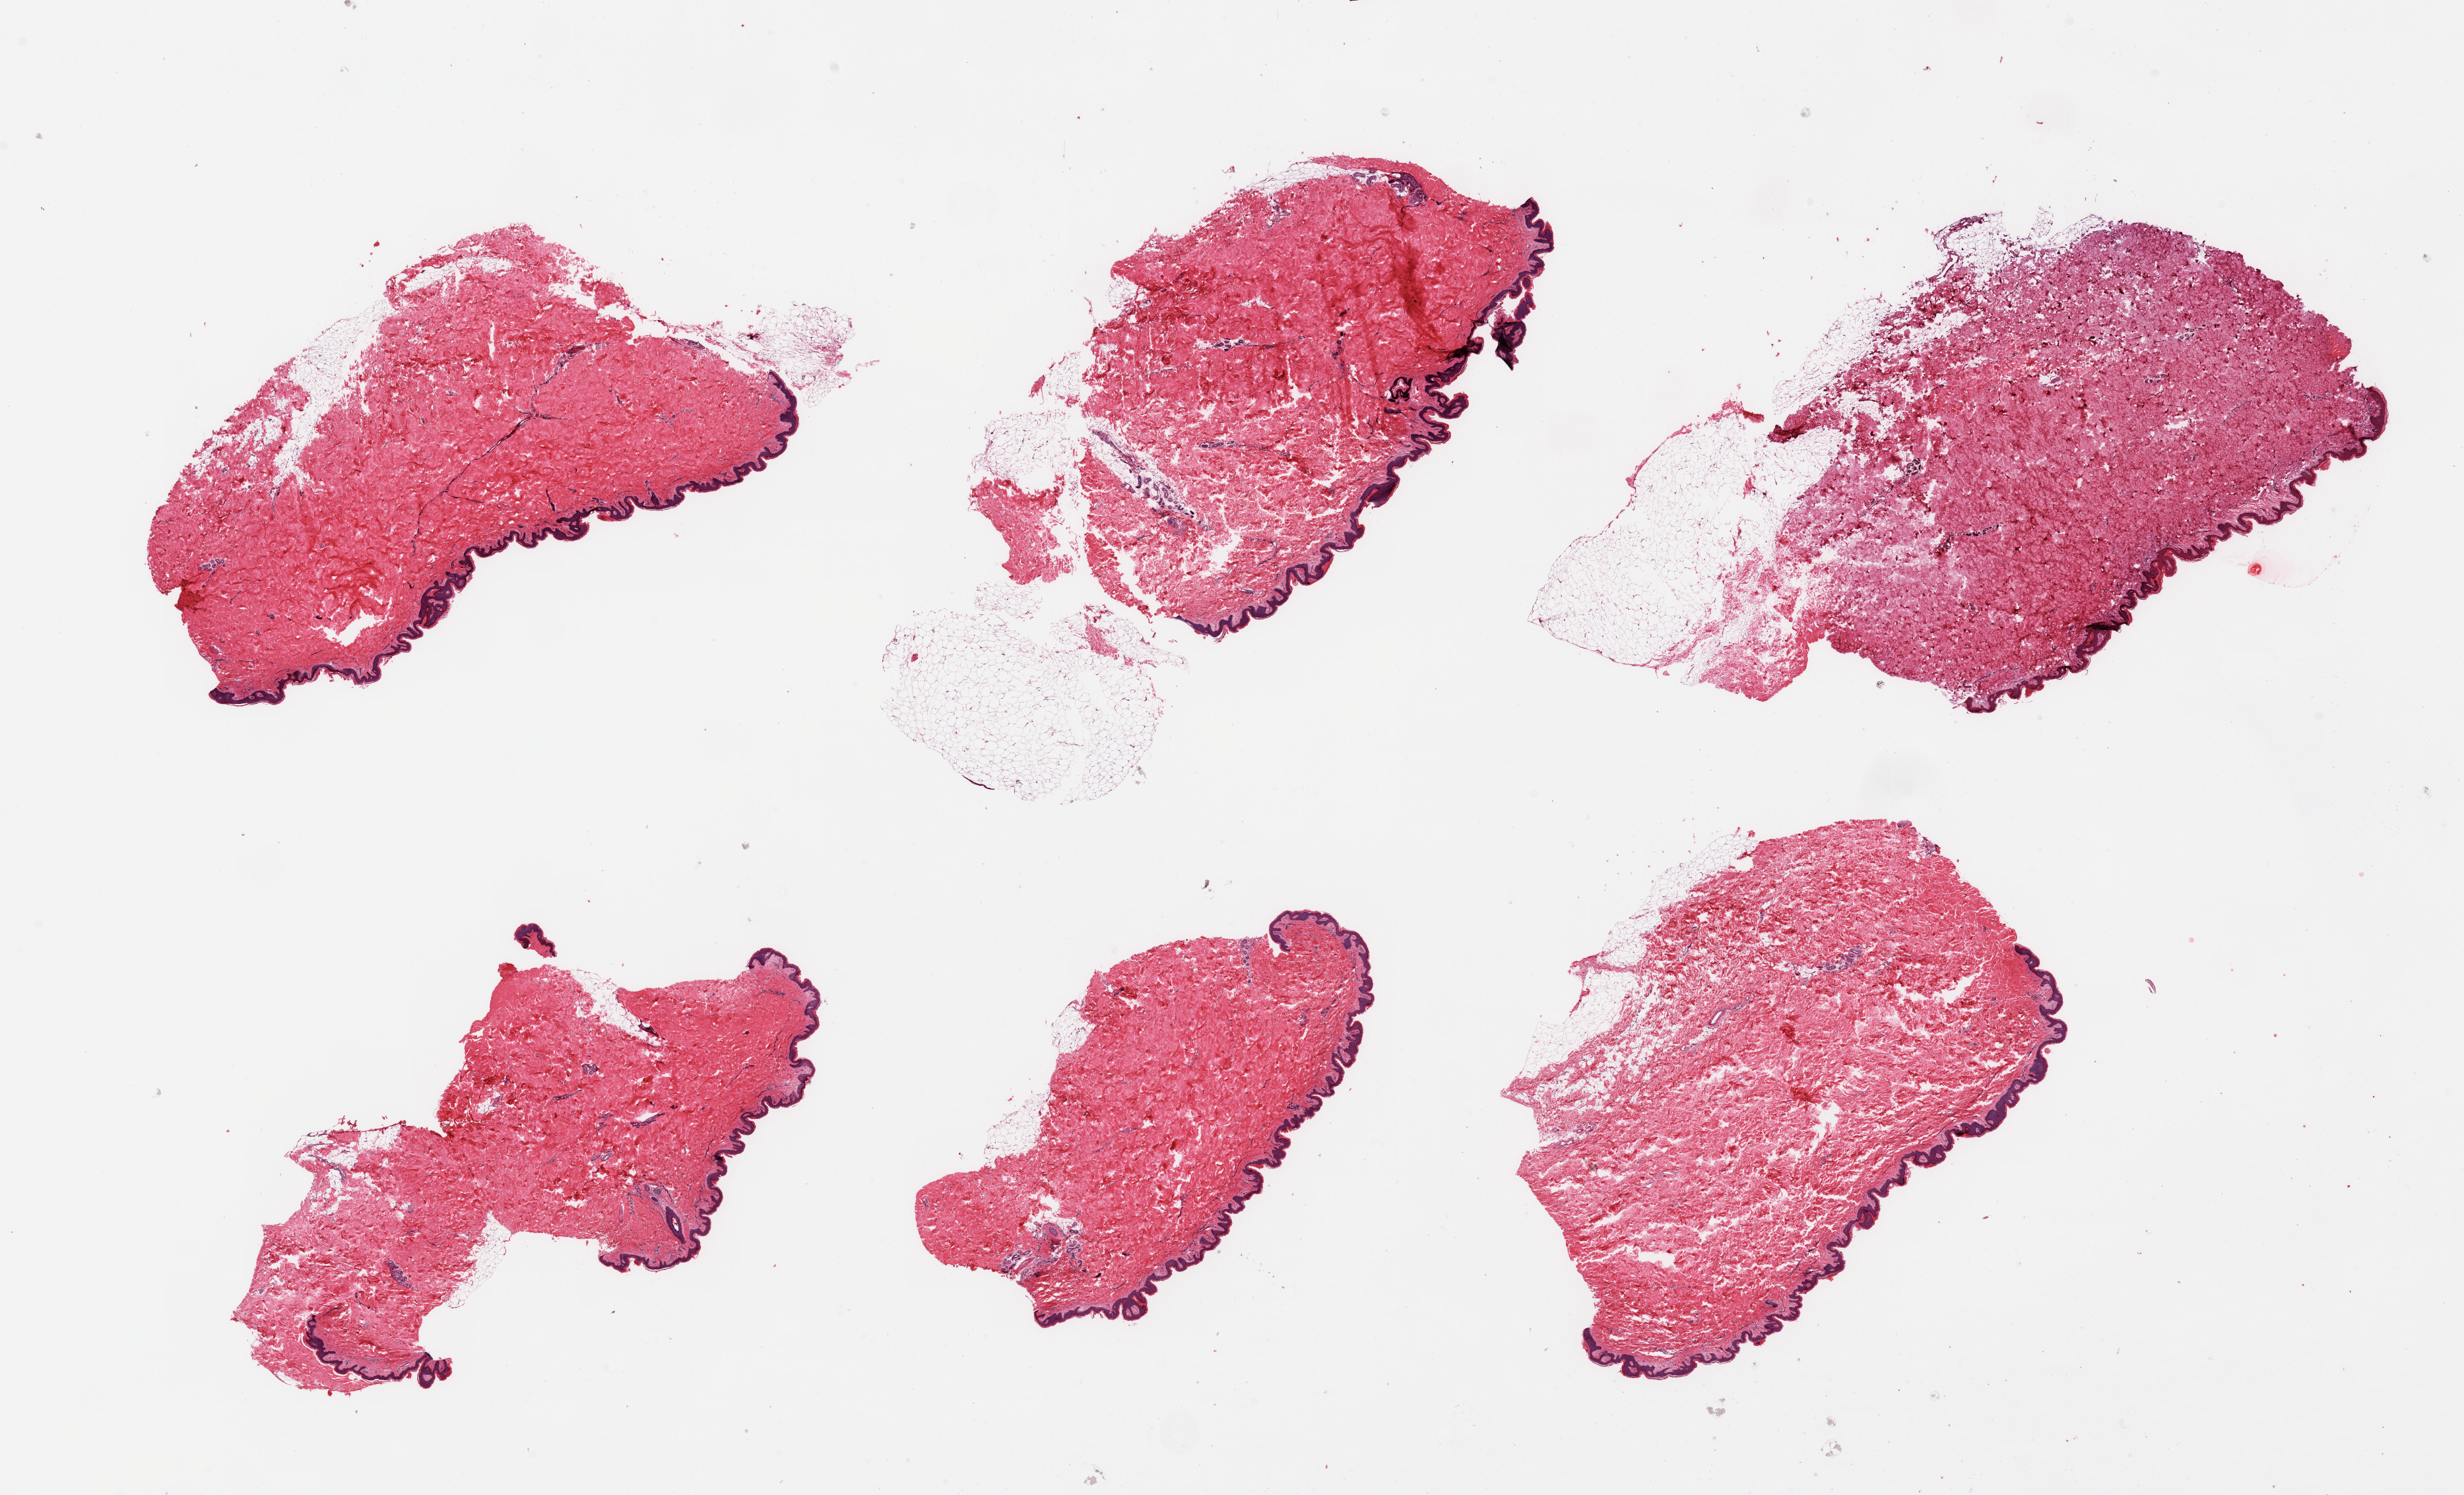
Digitized hematoxylin and eosin (H&E)-stained section — a low-resolution overview of the entire scanned area, about 29.5 x 17.9 mm. PAXgene-fixed paraffin-embedded (PFPE) section. Sampled site (target tissue): skin of suprapubic region. Tissue donor sample.
Review note (as recorded): 6 pieces; minimal dermal fat; focal untrimmed subcutaneous fat.